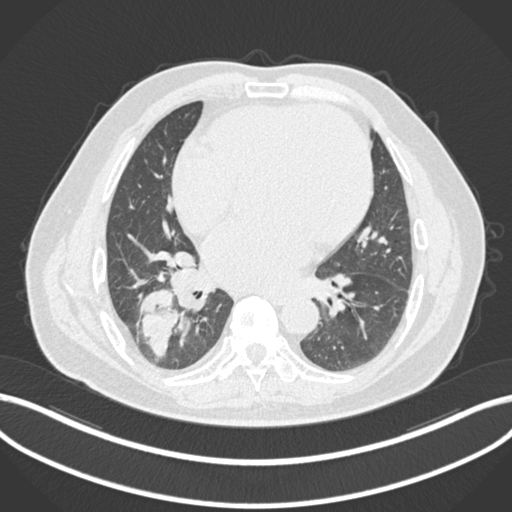
Chest CT, one axial slice. Slice 77 of 200 in the series (ordered by position). 120 kVp. Lung window (W 1500 / L -600 HU). 1 mm slice thickness. 512 × 512 image matrix, field of view 400 × 400 mm. Patient: male, 59 years.
Structures marked on this image (bounding box drawn by a radiologist):
- lung tumour (recorded histology: adenocarcinoma): box from (x=137, y=288) to (x=181, y=357) px